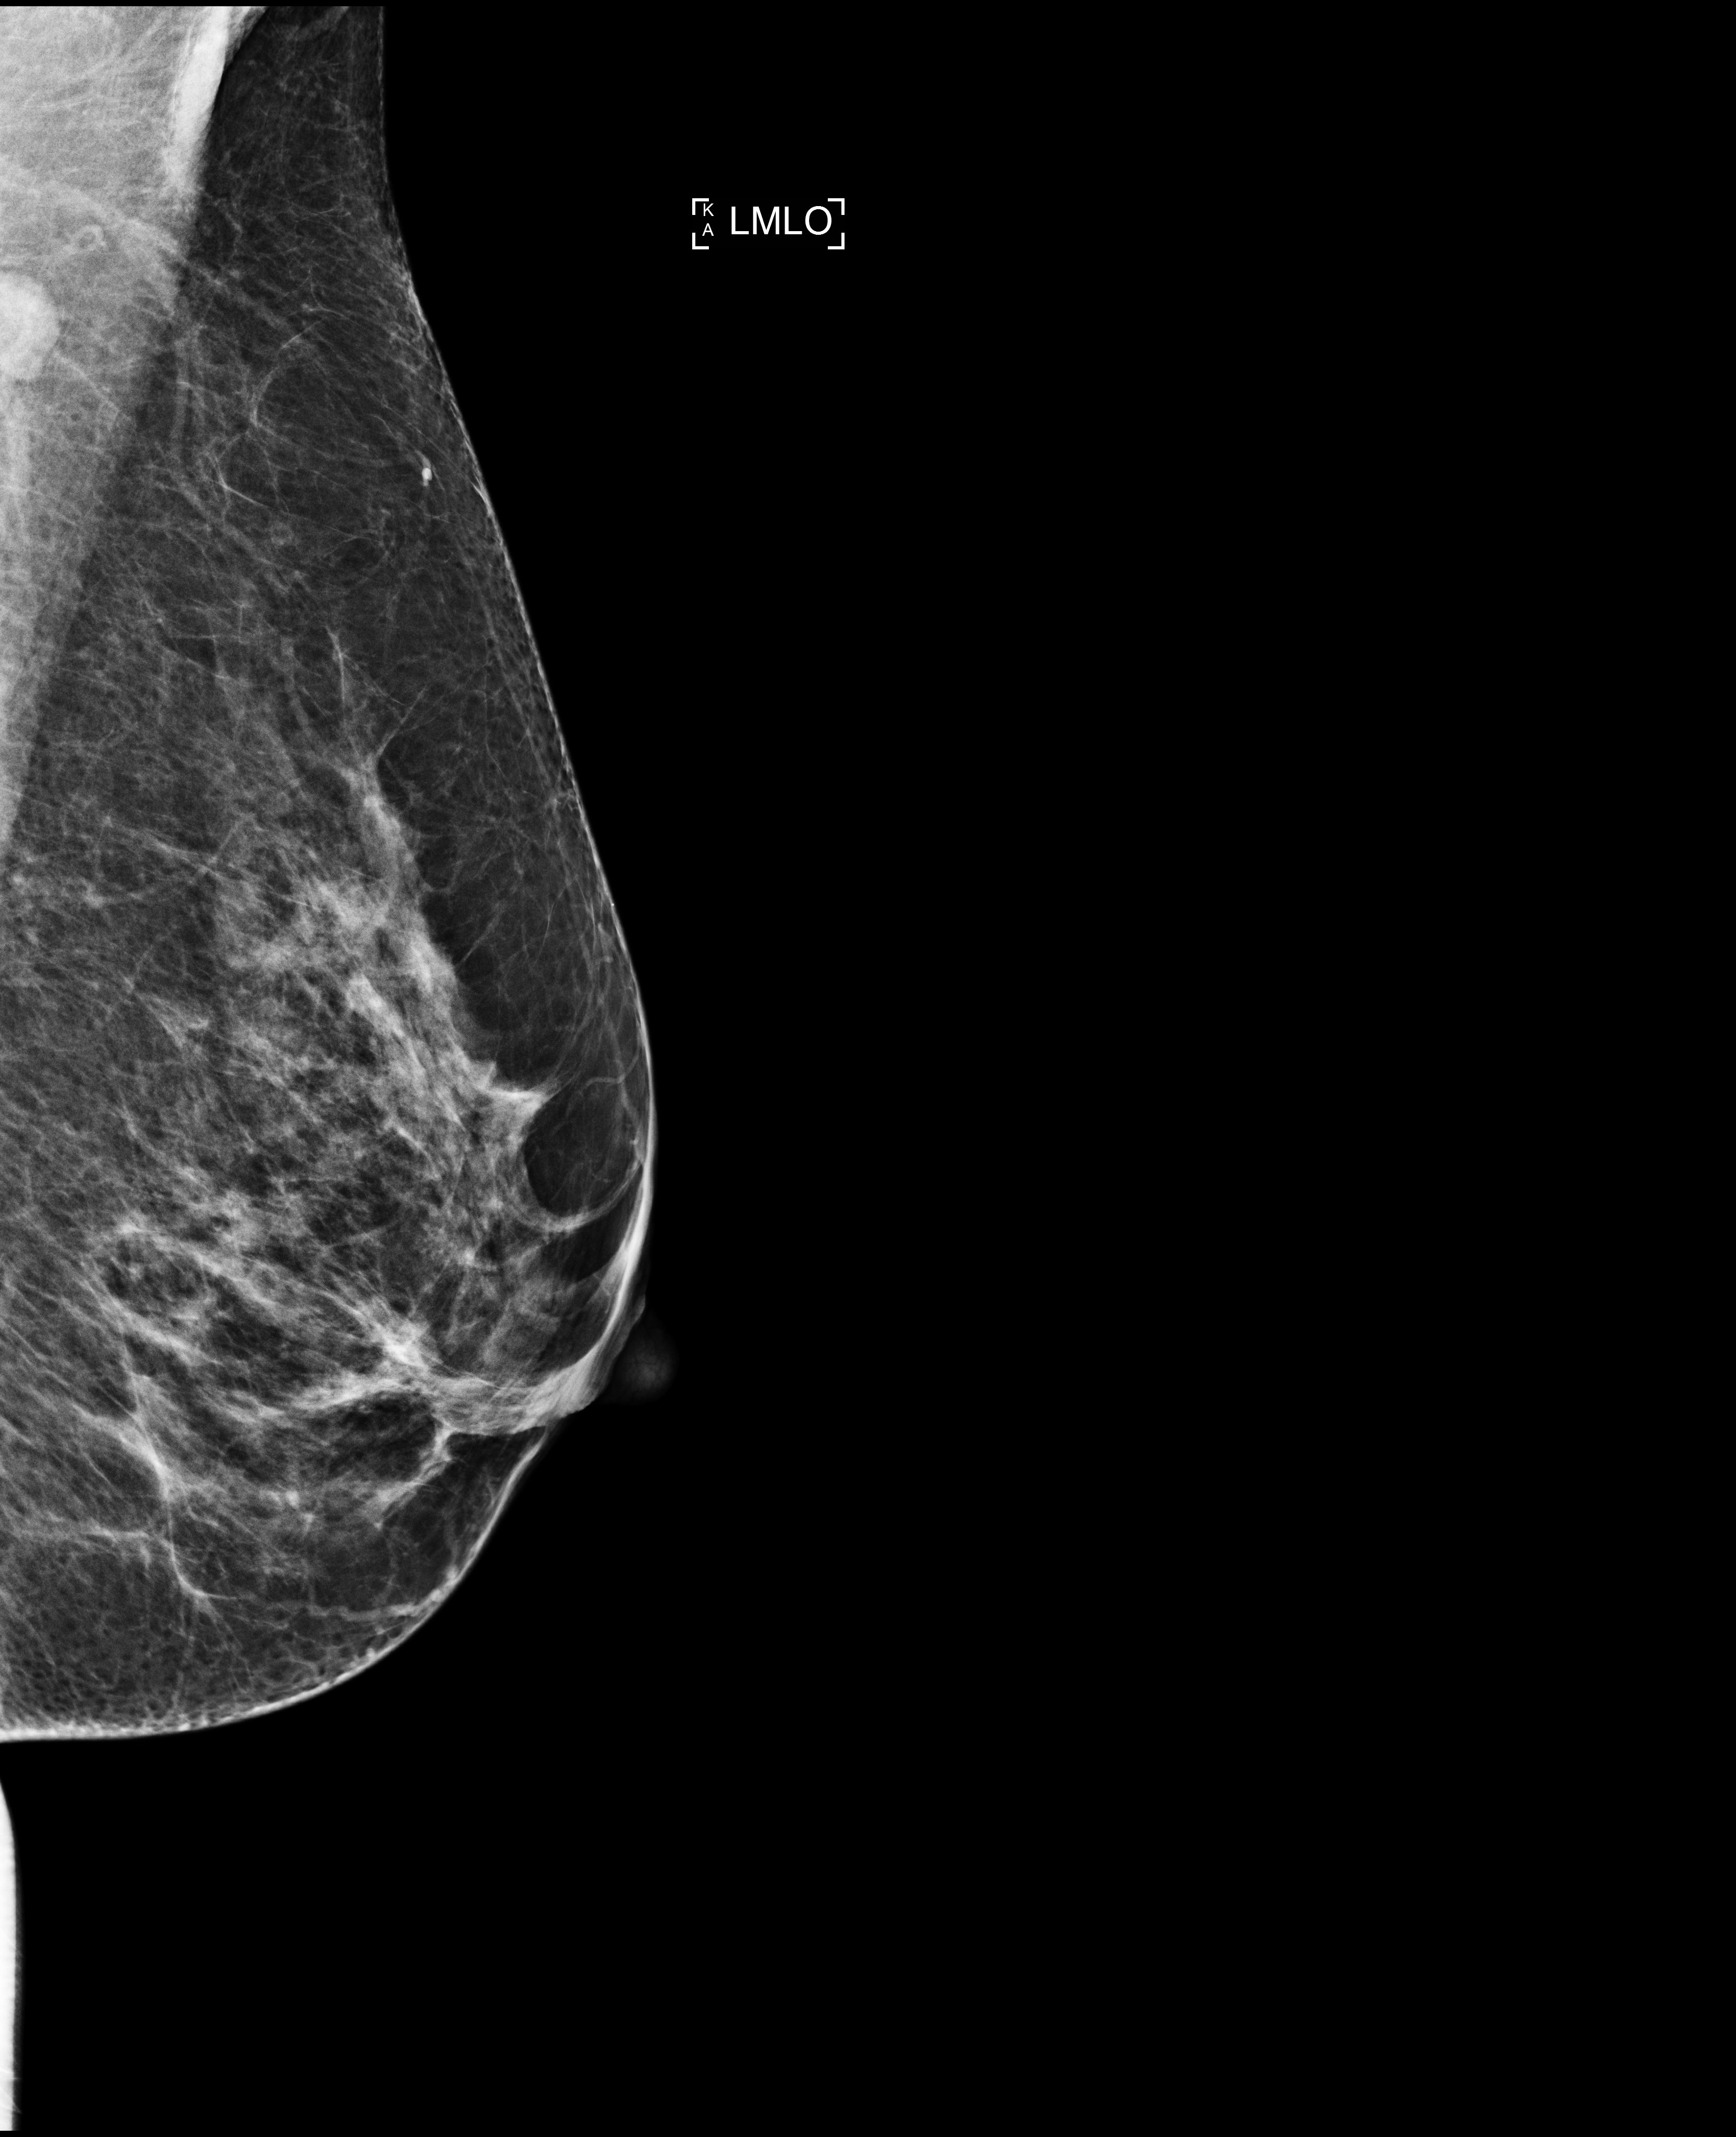
Annual screening mammography examination. Patient aged 52 years (female).
Image type: full-field digital mammogram. Breast: left. Projection: medio-lateral oblique projection.